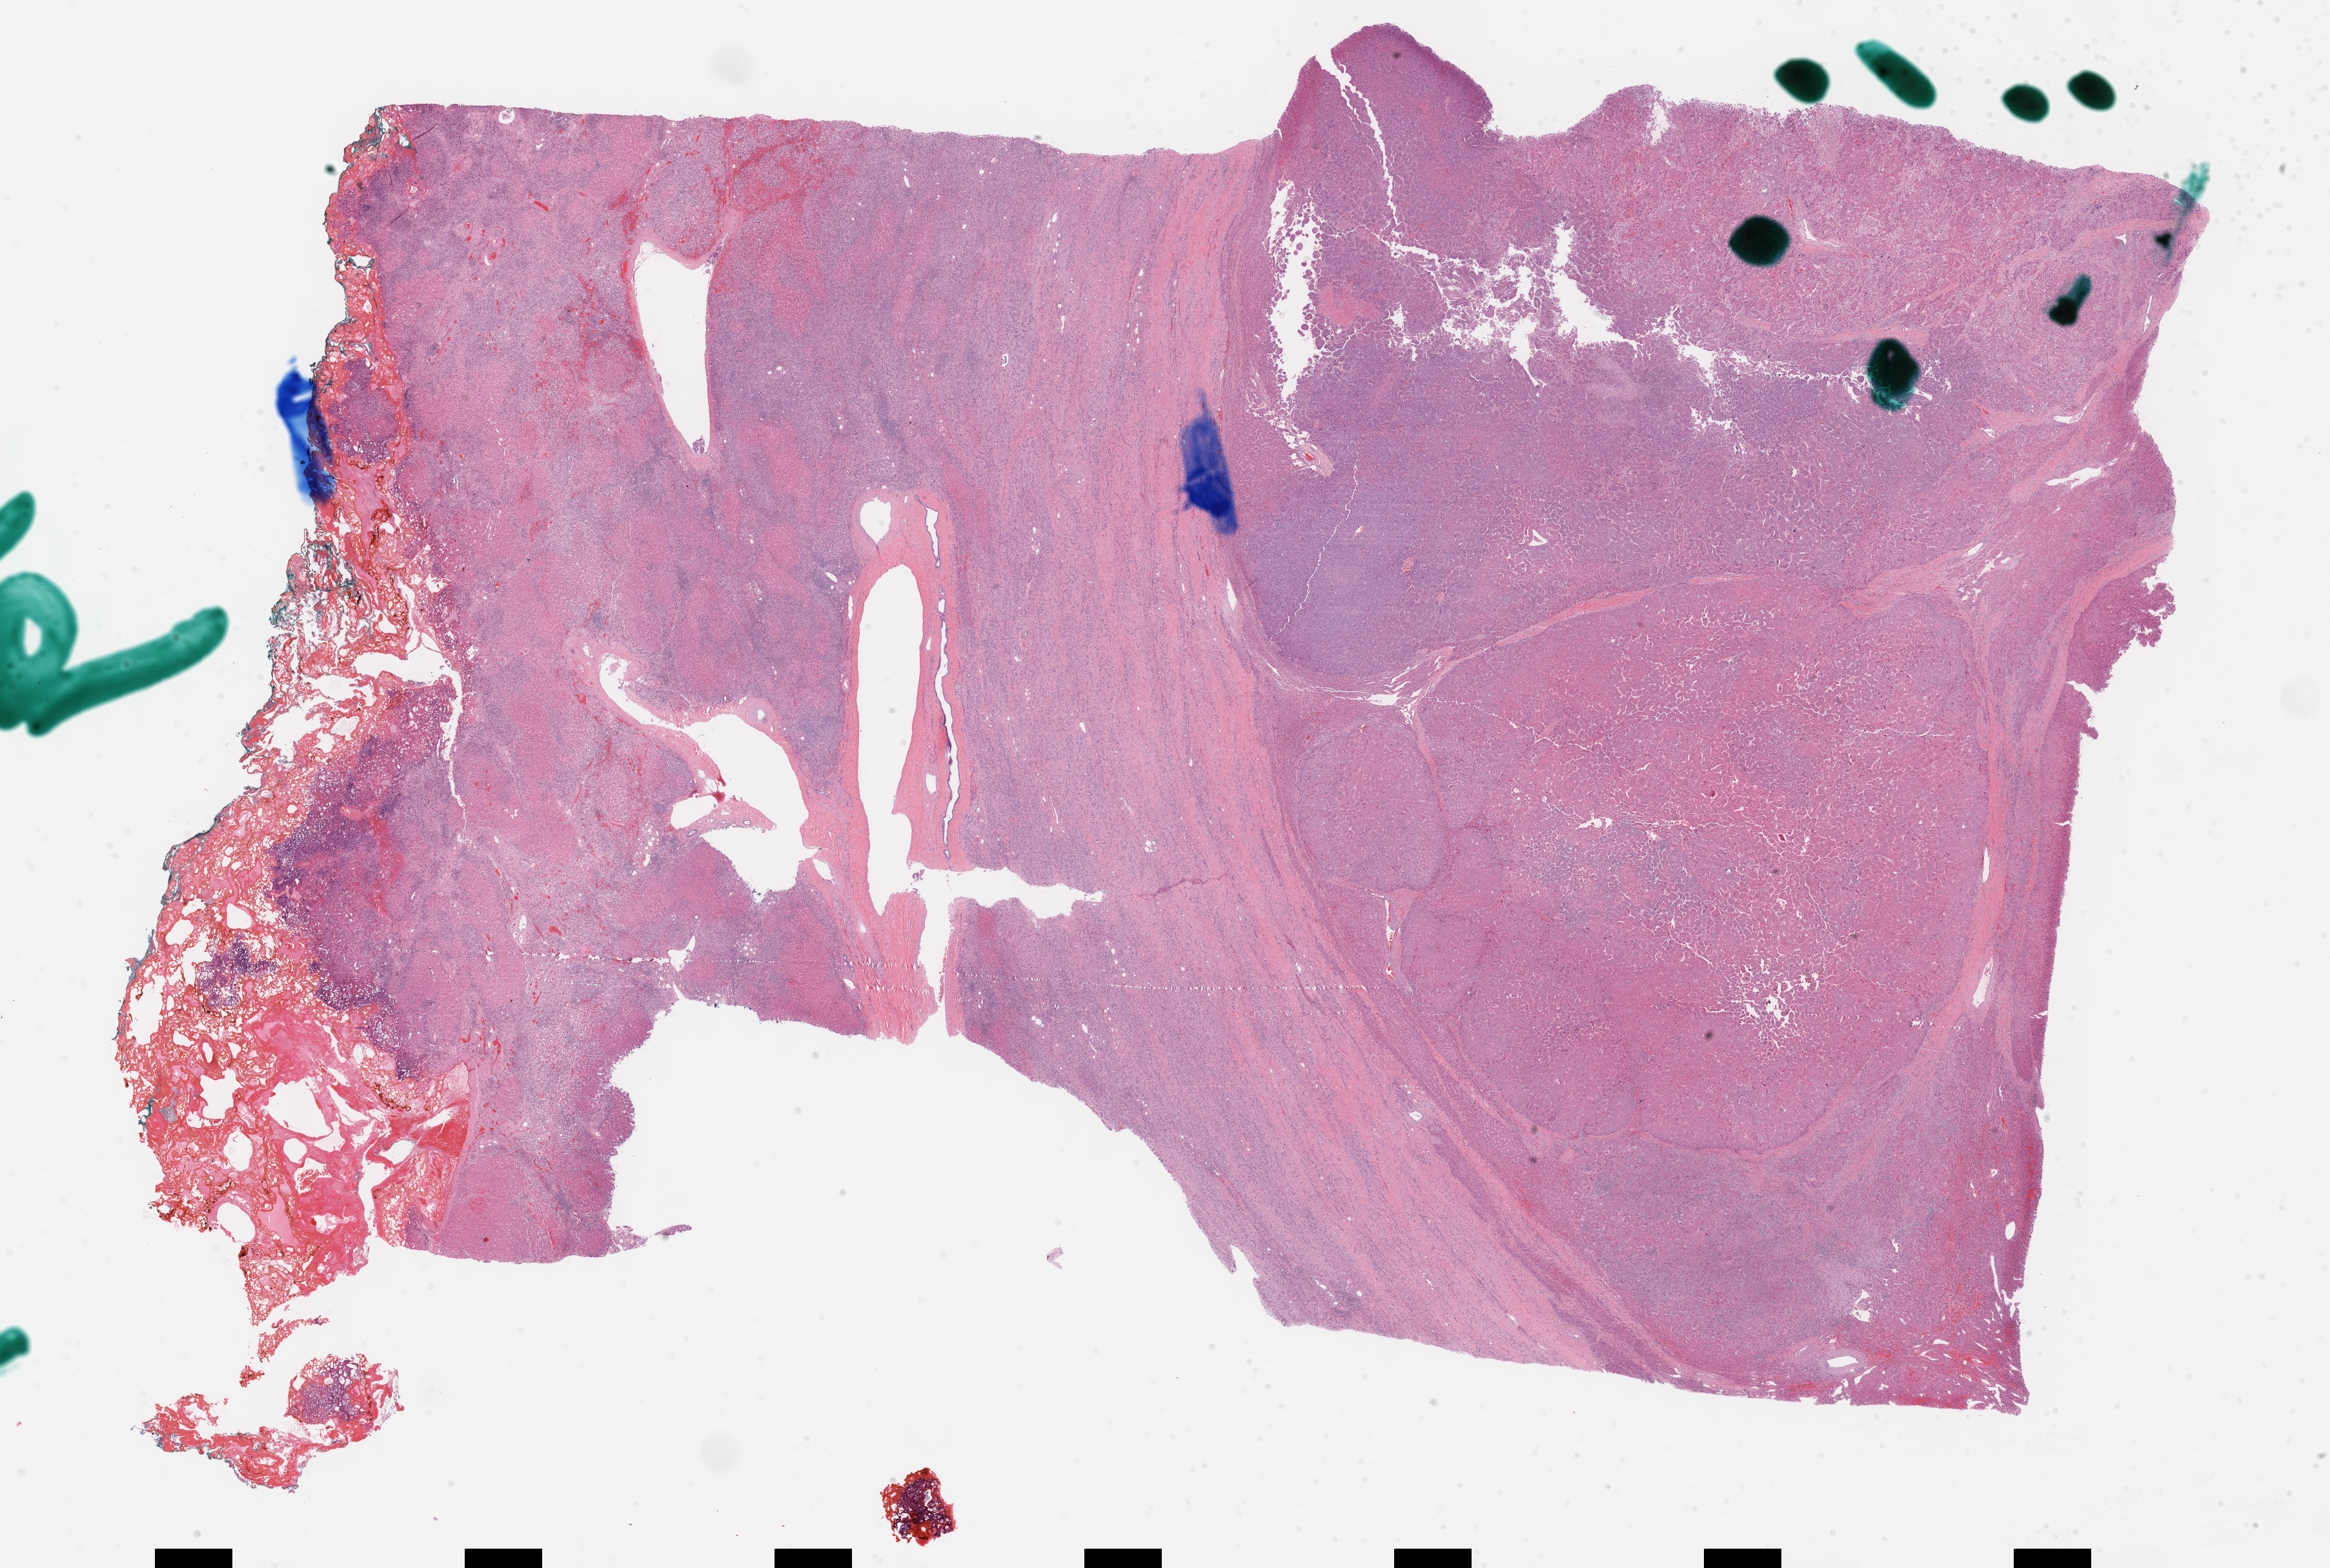
Hematoxylin and eosin (H&E) stained whole-slide image — low-resolution overview of the scanned area, about 29.2 x 19.7 mm, FFPE section, sample: primary tumour, liver. Patient: male, age at initial diagnosis 67 years. Histologic grade: G3 (poorly differentiated).
* AJCC pathologic stage: I (7th edition)
* diagnosis: Hepatocellular carcinoma, NOS